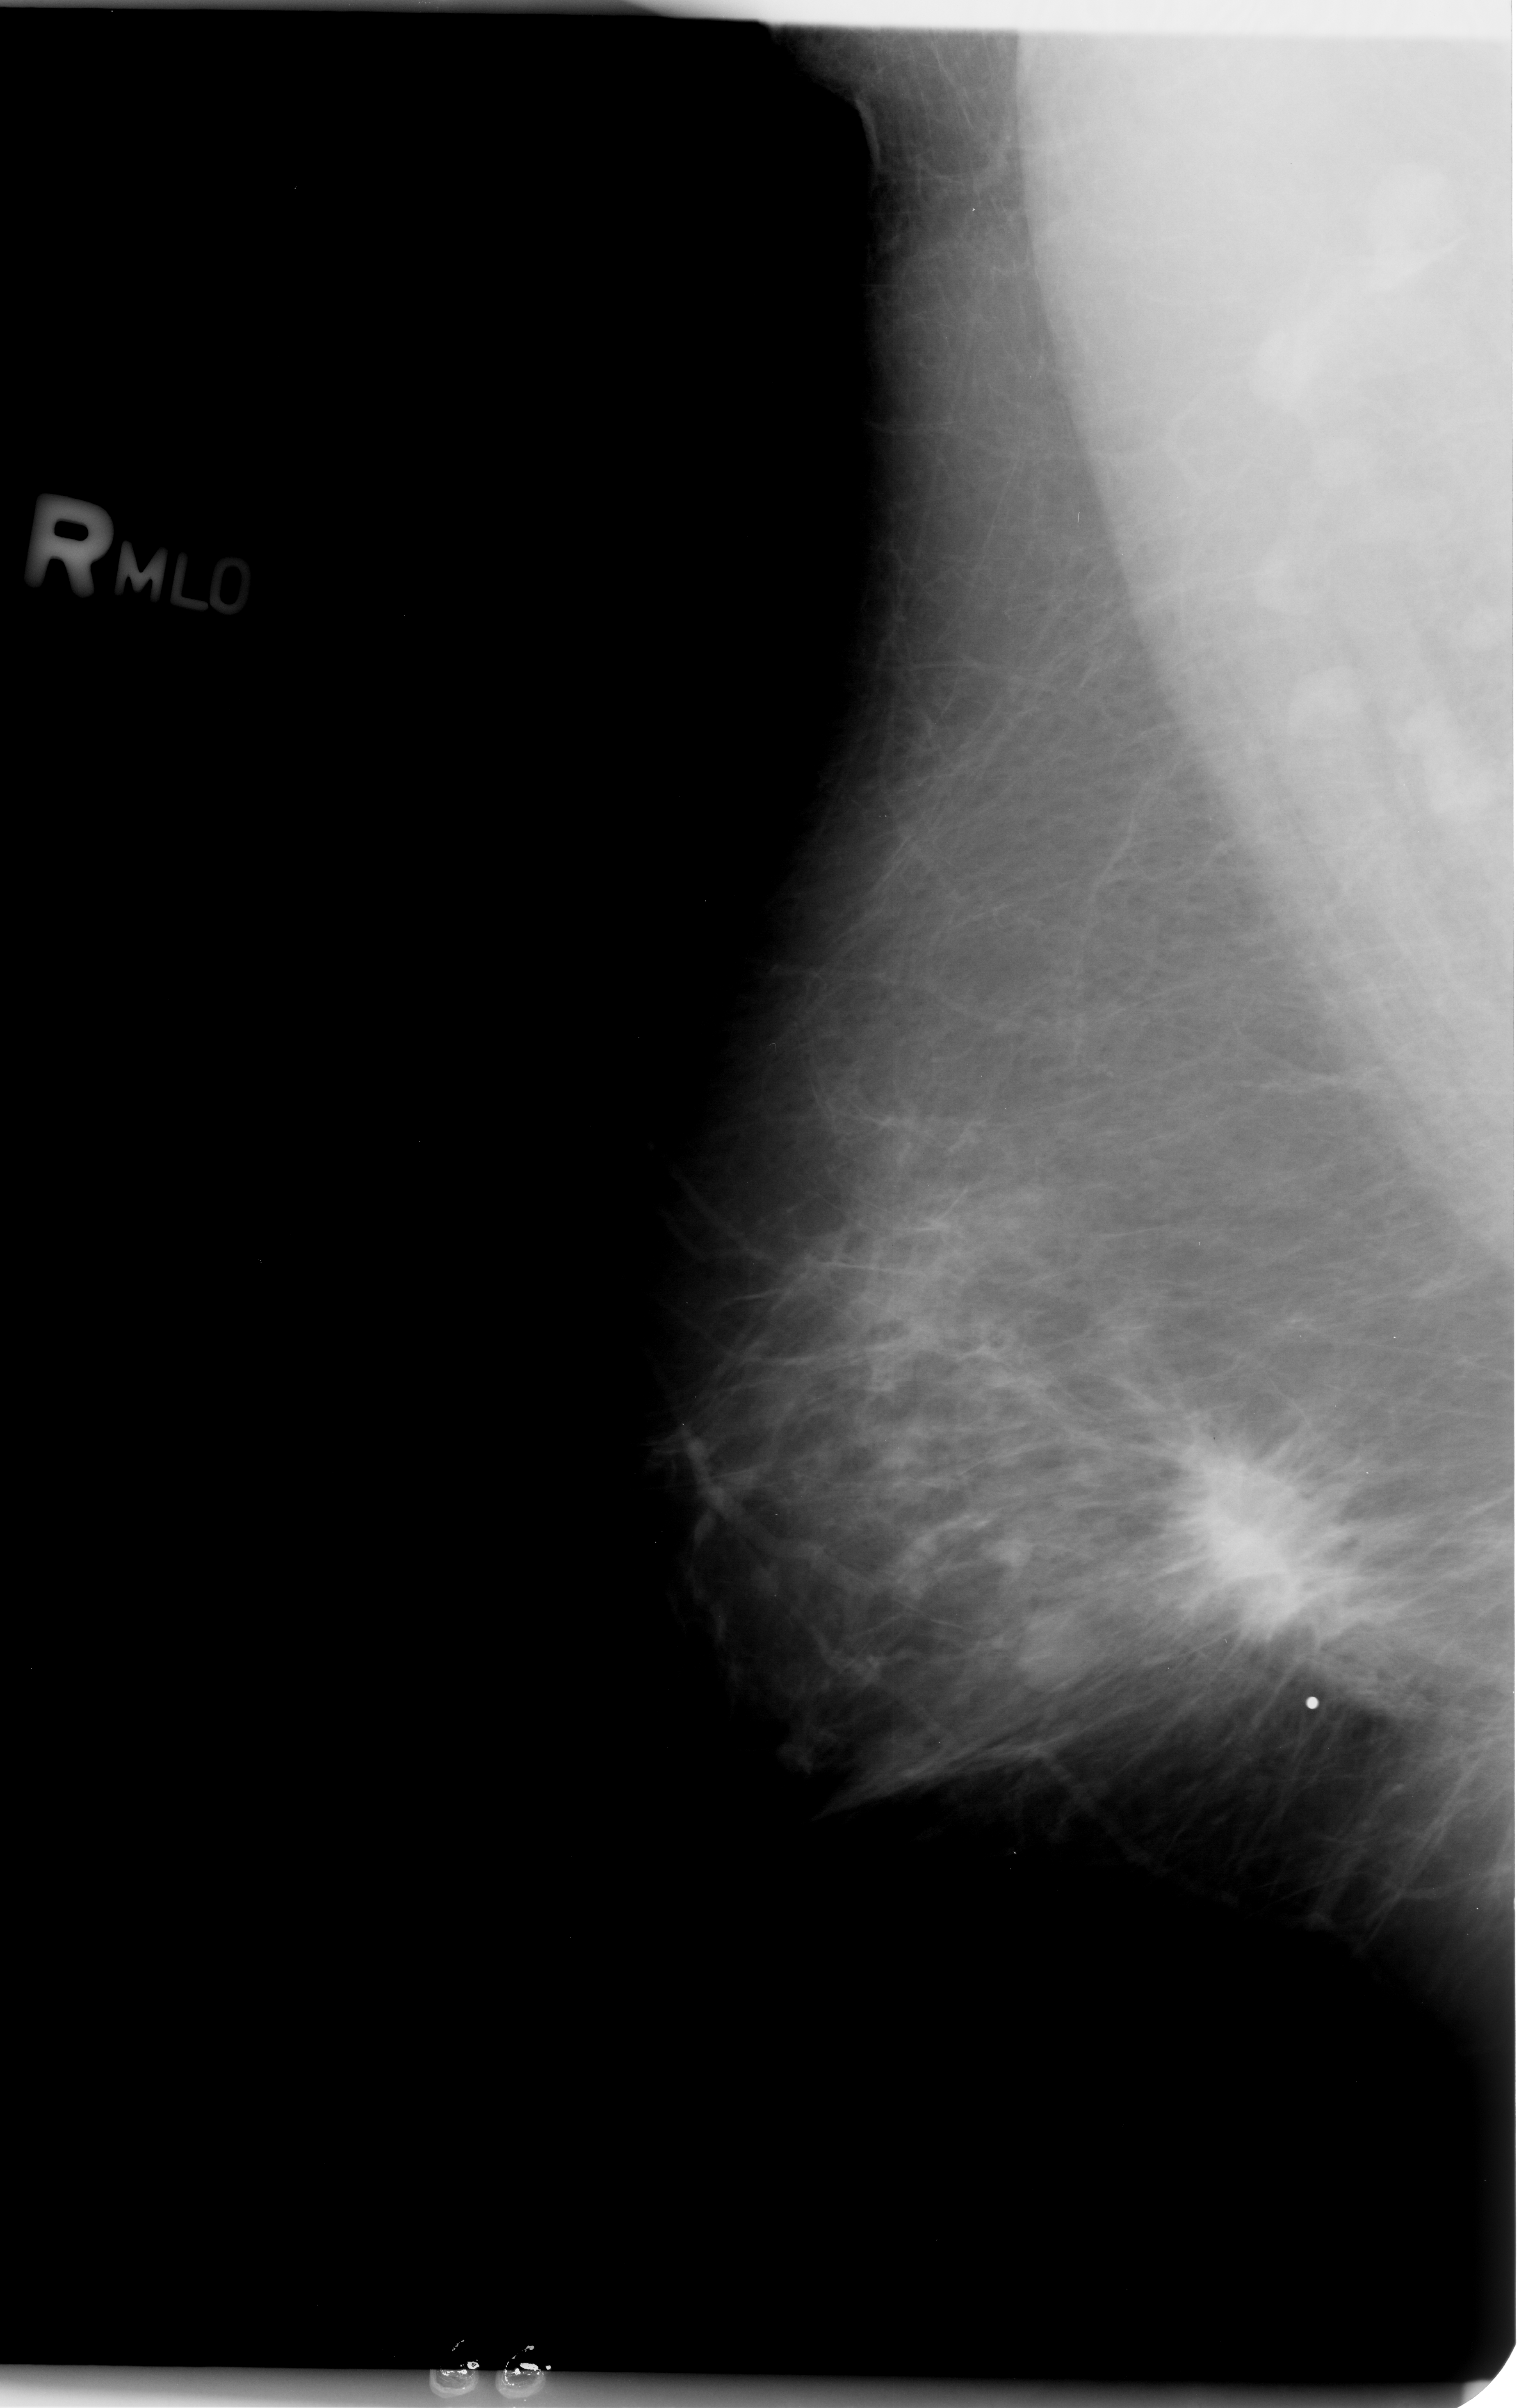
Scanned film-screen mammogram, right breast, MLO view, BI-RADS breast density category 2 (scale 1–4).
Mass, shape irregular / architectural distortion, margins spiculated; BI-RADS assessment category 5; pathology result (as recorded, not read from the image): malignant.